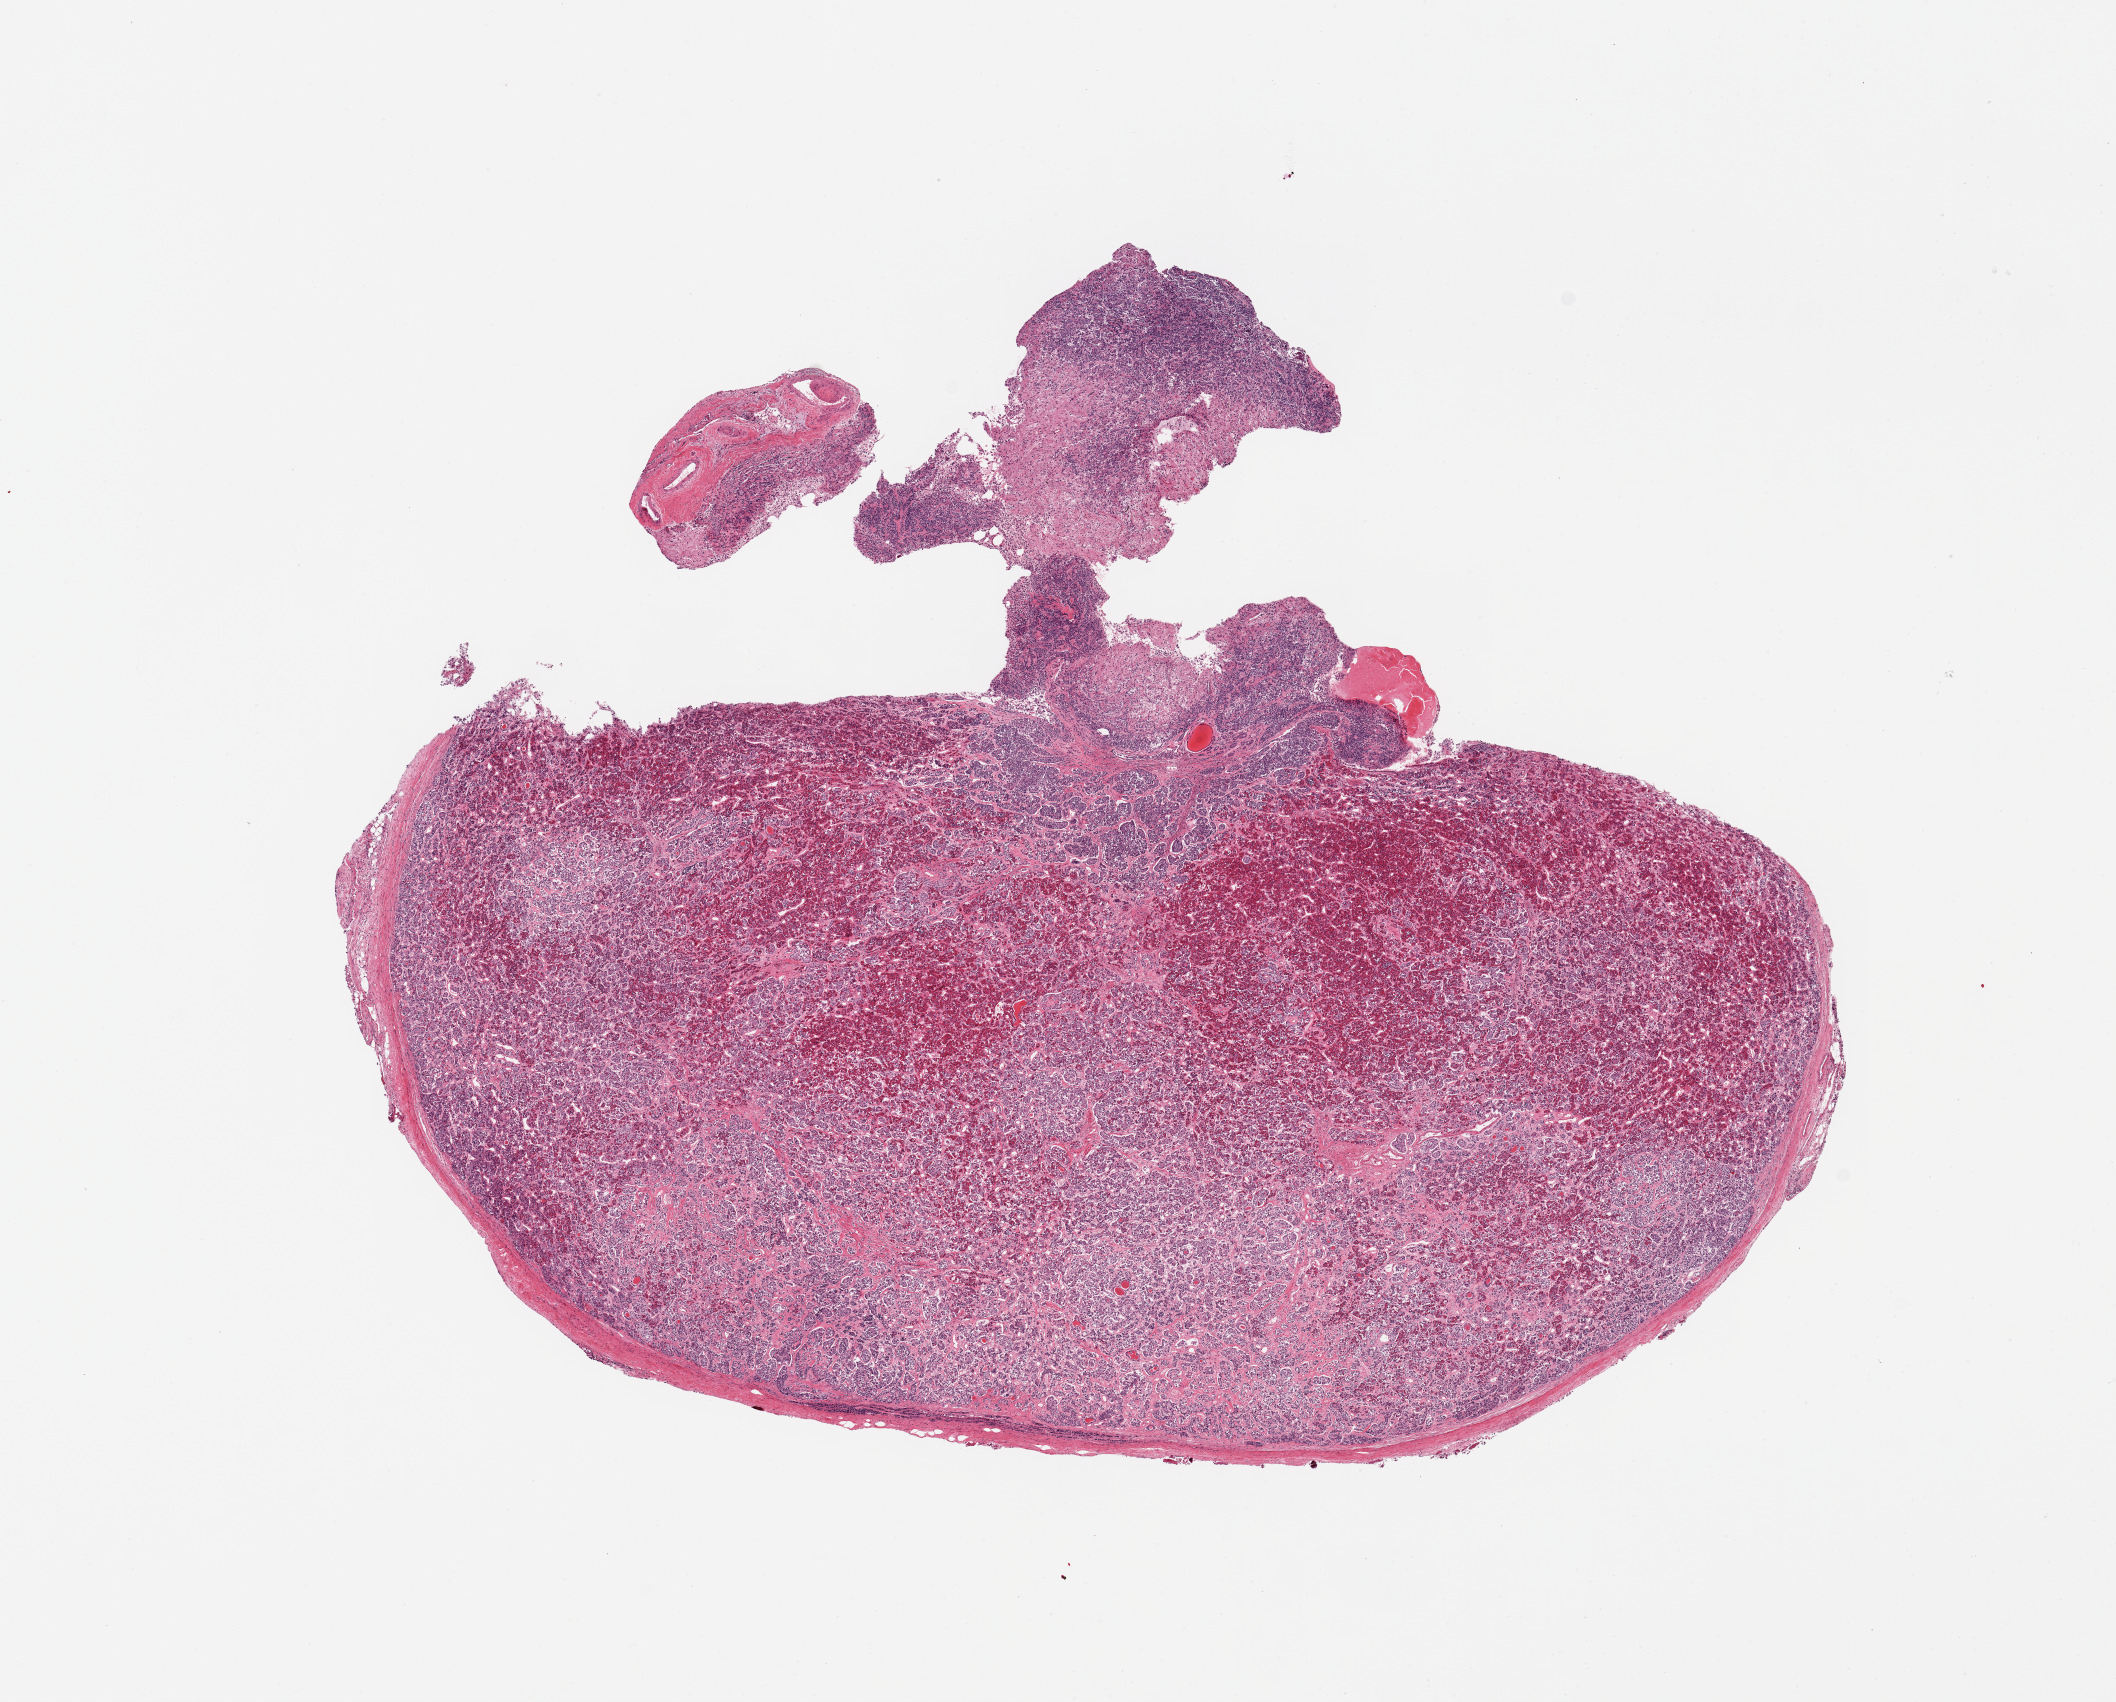
Digitized haematoxylin and eosin-stained section — a low-resolution overview of the entire scanned area, about 16.7 x 13.5 mm; PAXgene-fixed, paraffin-embedded tissue; target tissue: pituitary; tissue donor sample.
• reviewer comment on this tissue sample: 1 pieces; mostly adenohypophysis with smaller portion of neurohypophysis